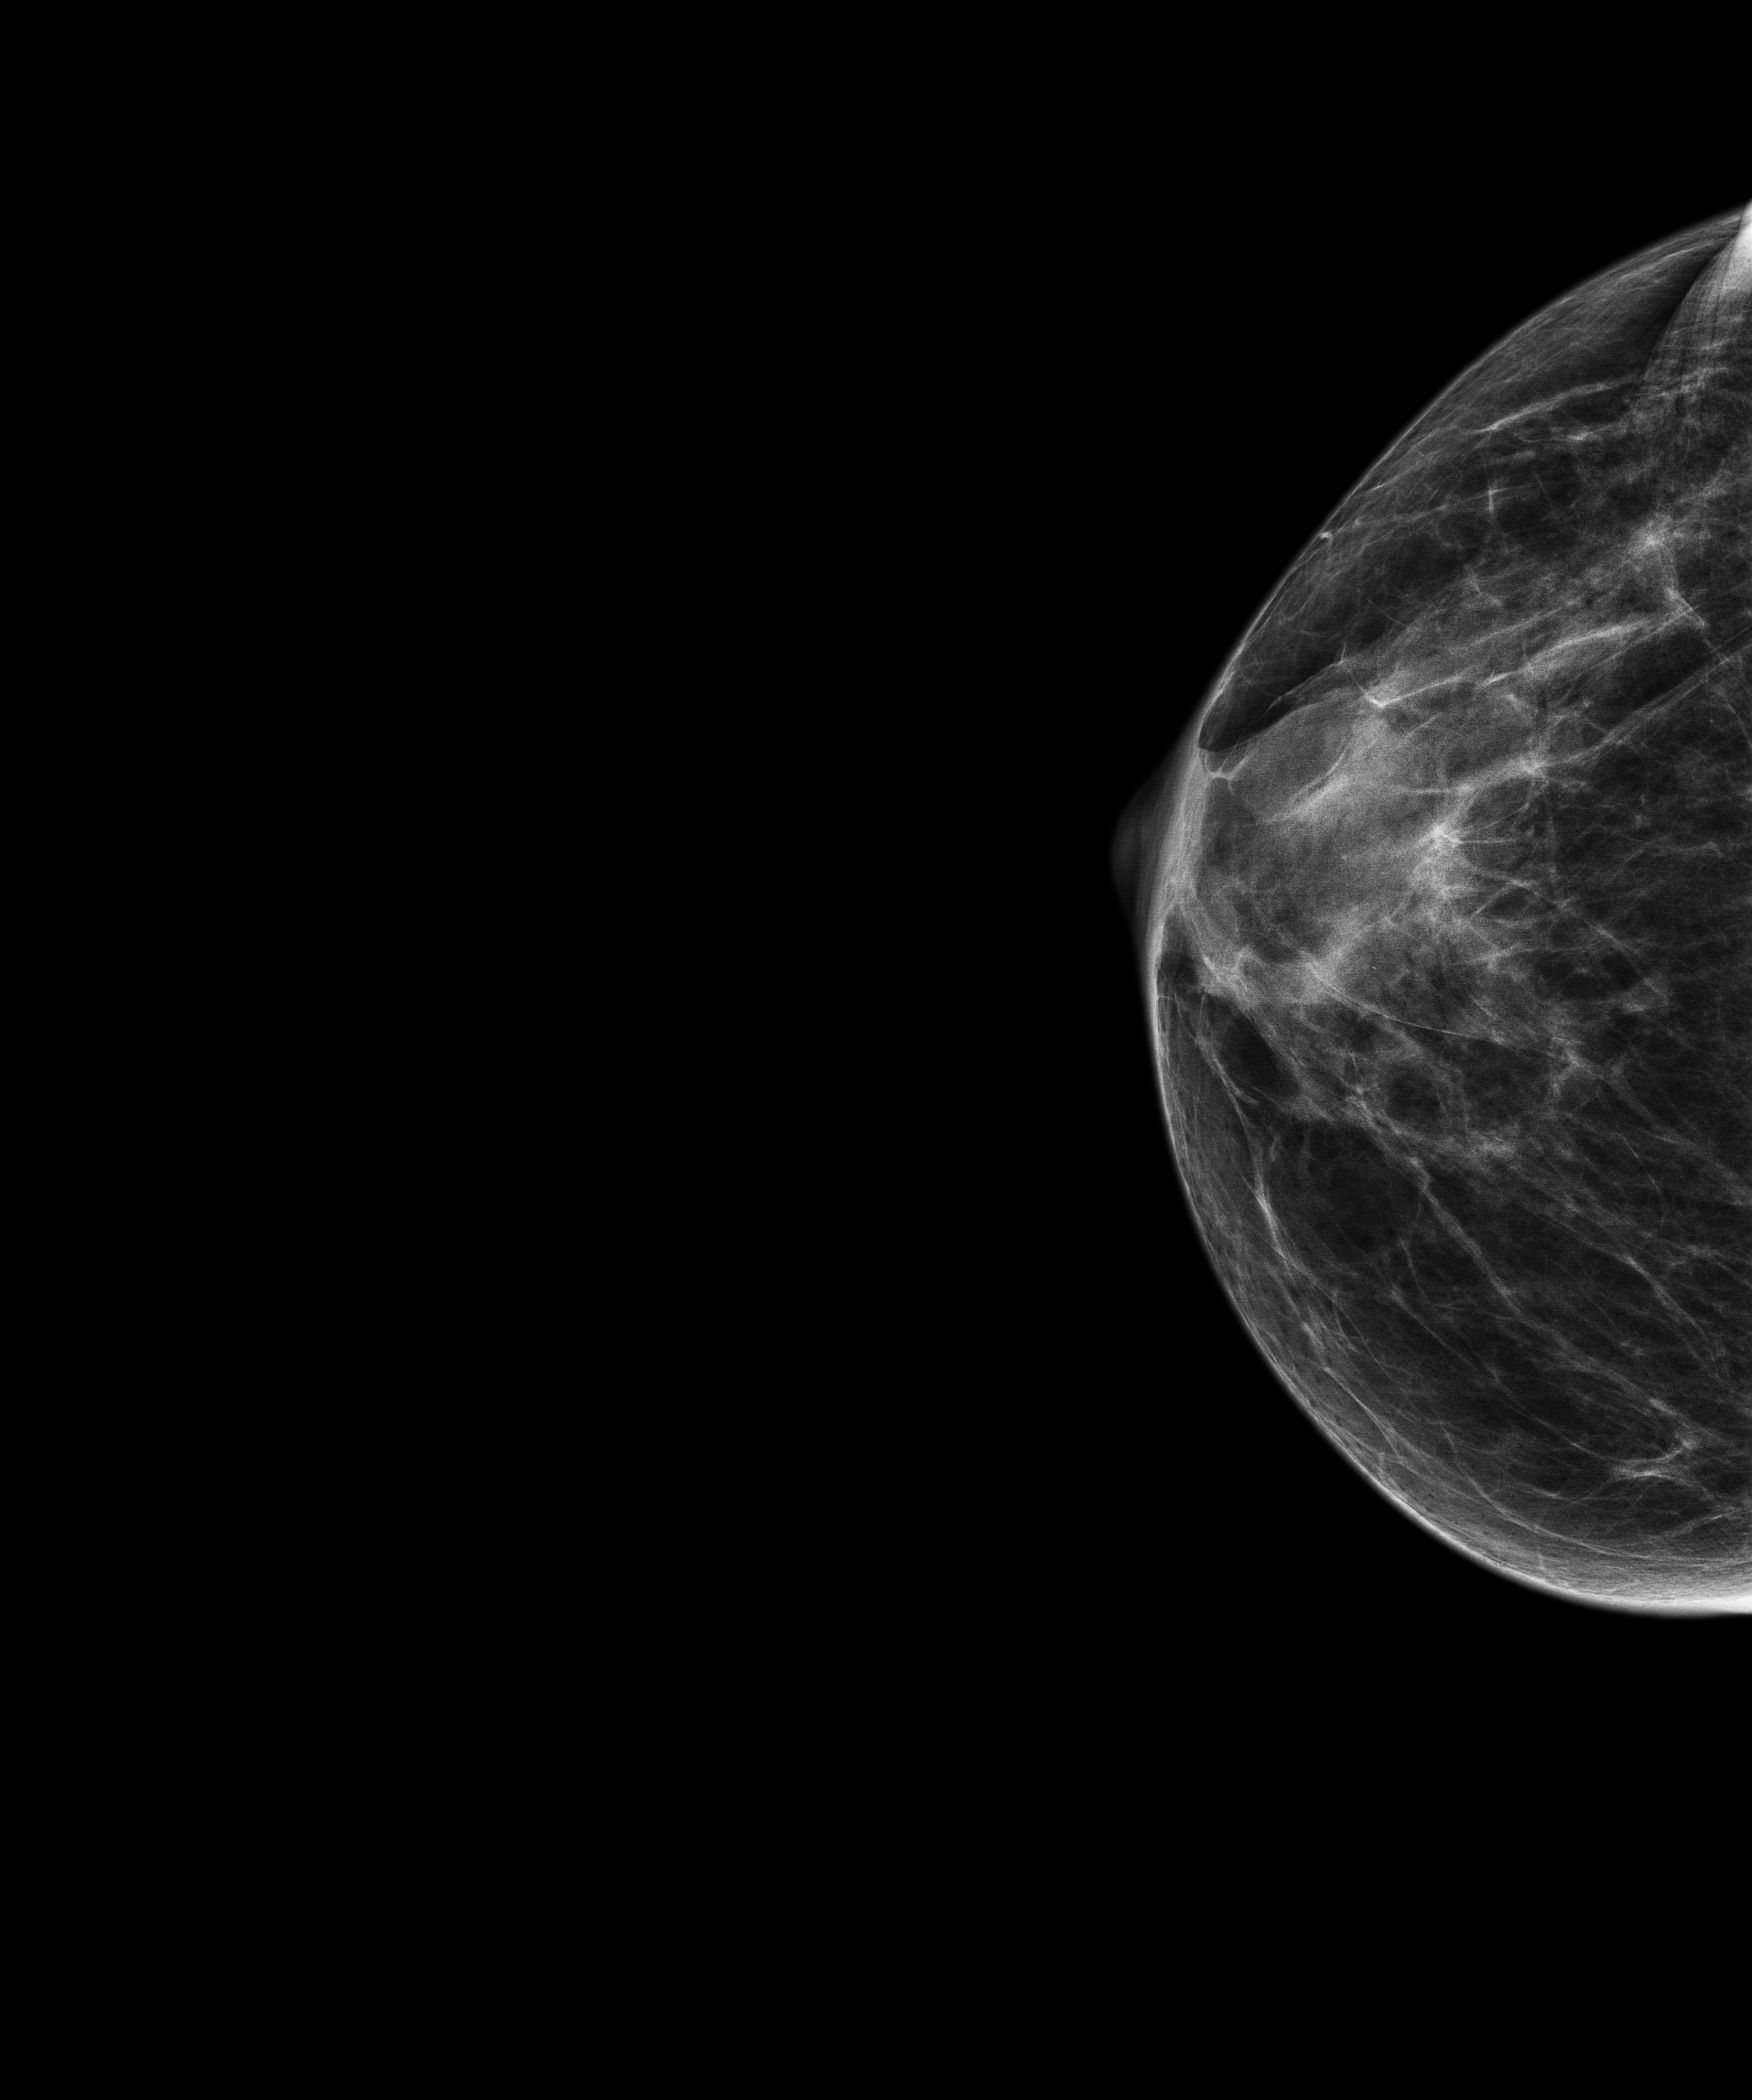
Annual screening mammography examination, compressed breast thickness 41.8 mm. Patient: female, 66 years.
Image type: full-field digital mammogram. Breast: right. Projection: cranio-caudal projection.